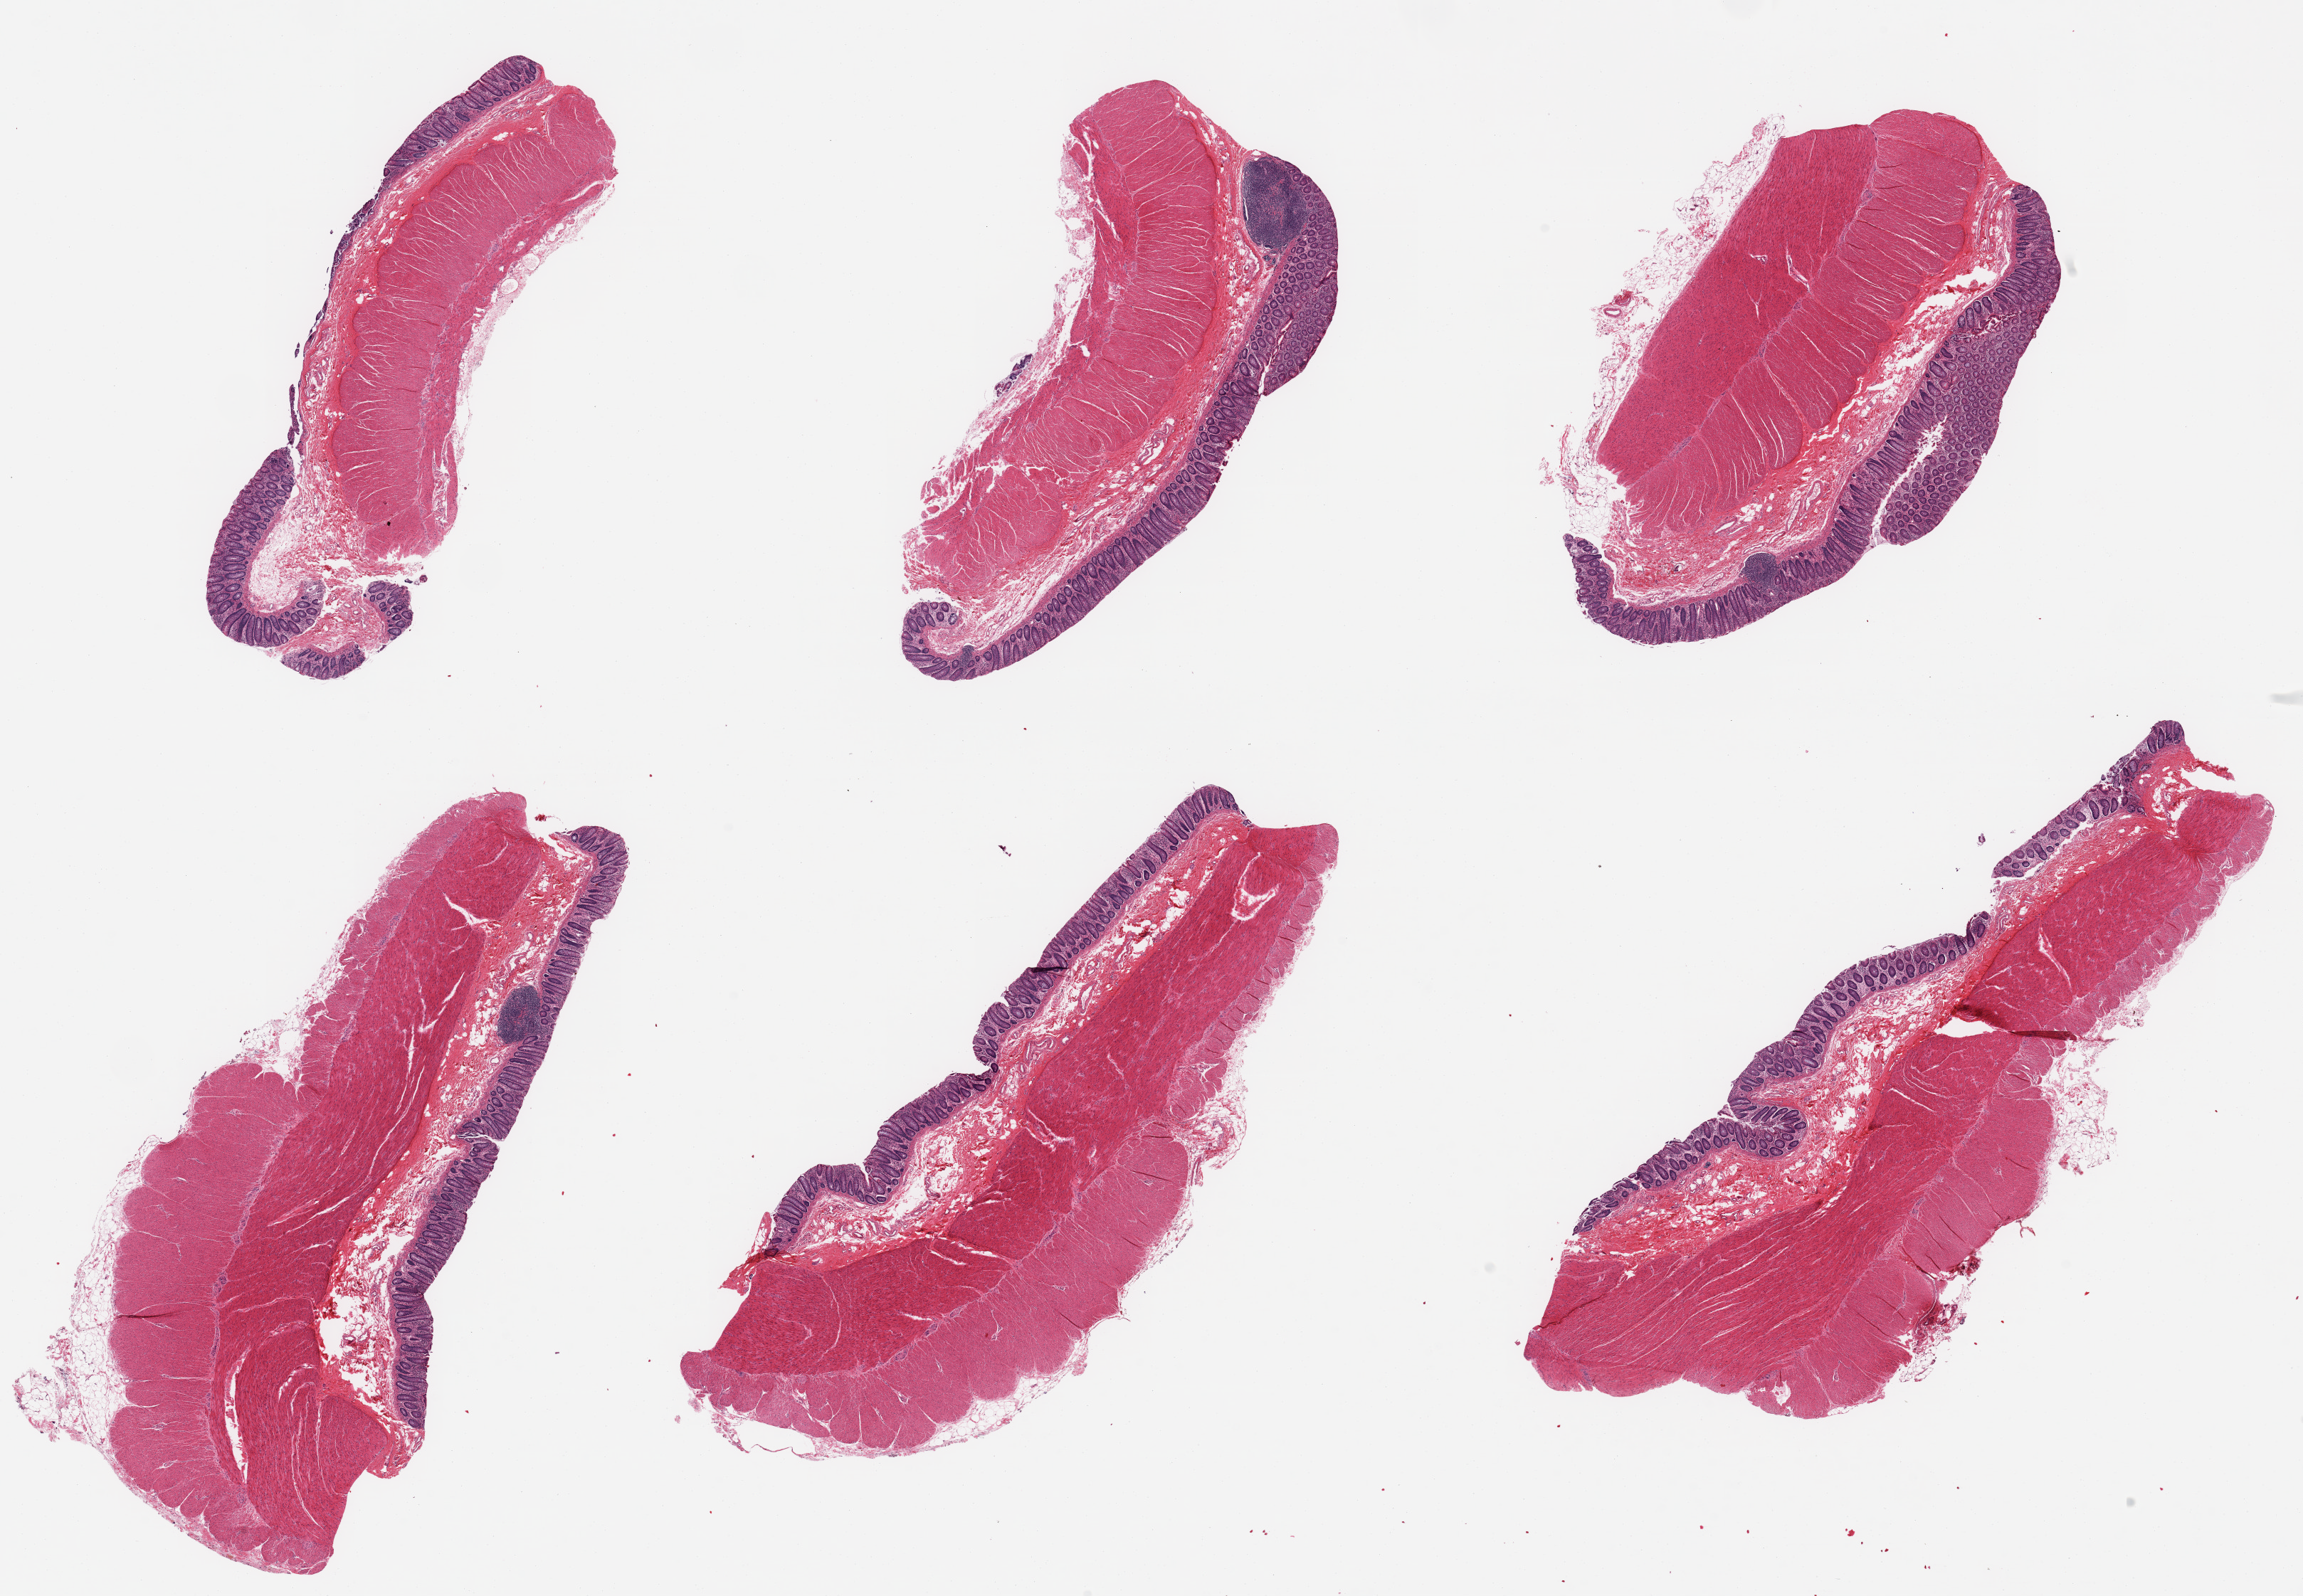
Digitized hematoxylin and eosin (H&E)-stained section — whole scanned area (about 25.6 x 17.7 mm, acquisition: 20x scan) shown as a low-resolution overview. PAXgene-fixed paraffin-embedded (PFPE) section. Section of transverse colon (target tissue). Tissue donor sample.
Pathologist's review note for this sample: 6 pieces; full thickness sections.